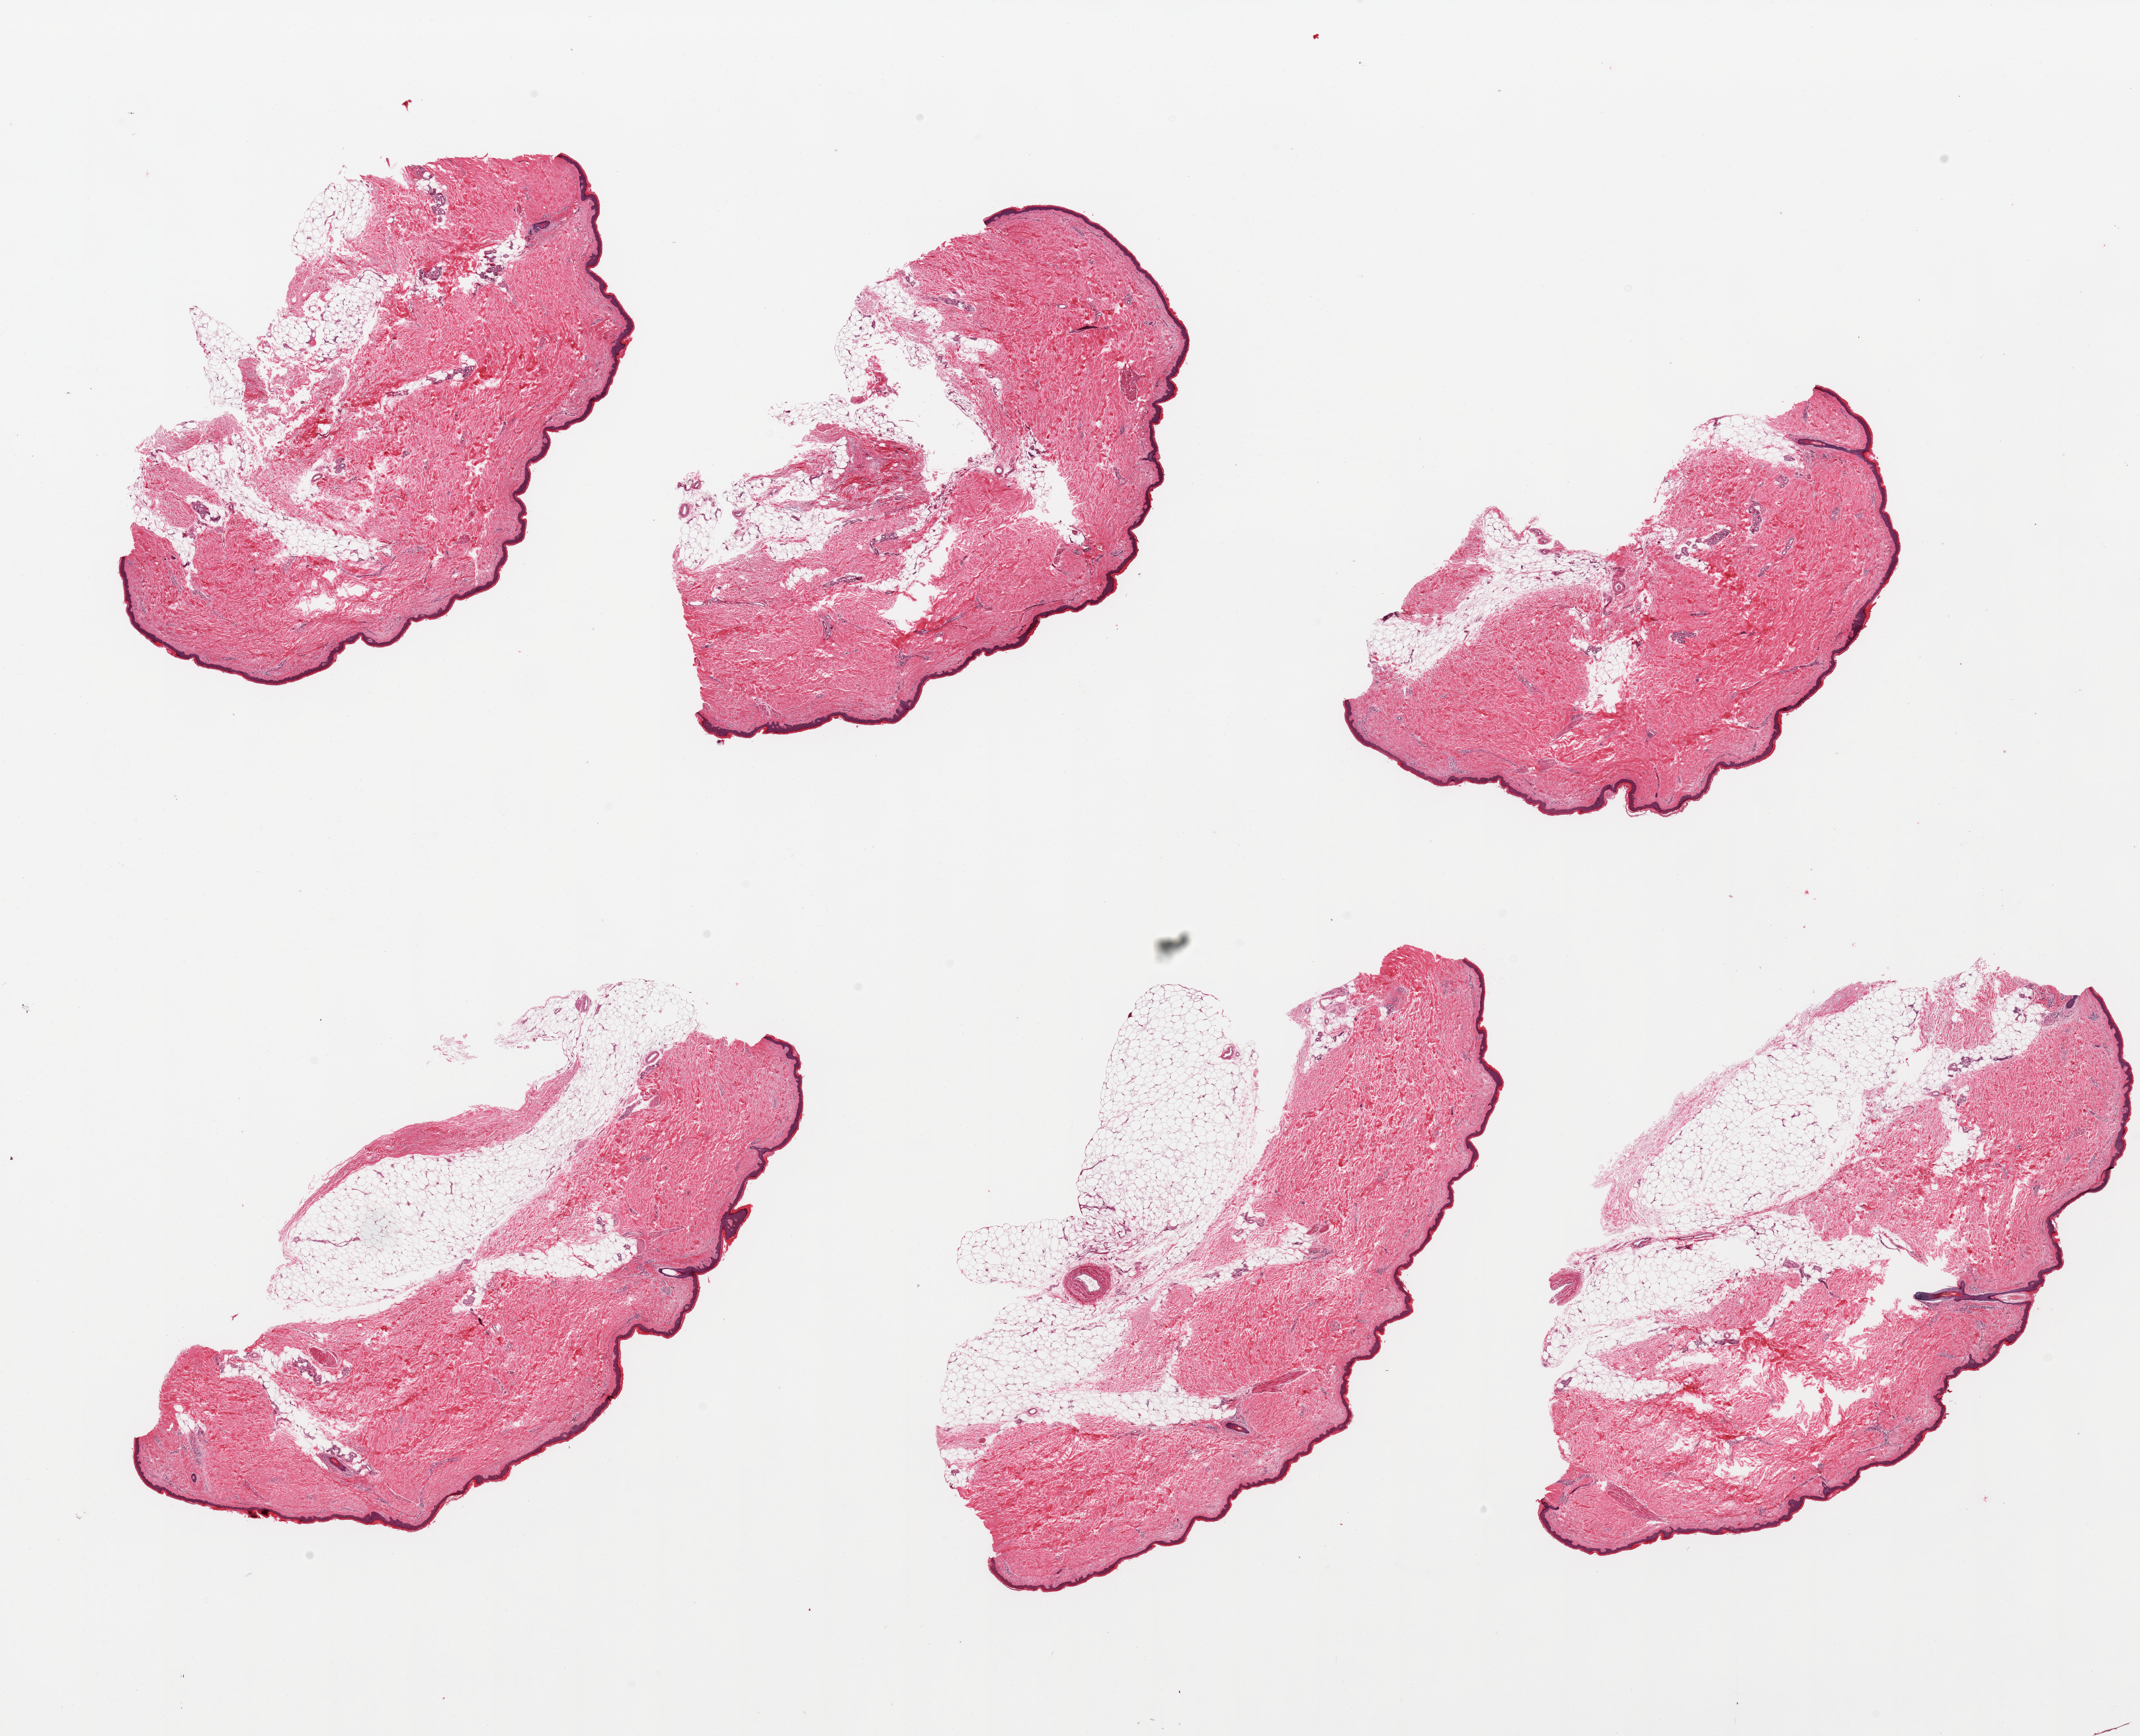
Digitized haematoxylin and eosin-stained section — low-resolution overview of the scanned area, about 25.6 x 20.8 mm; PAXgene-fixed paraffin-embedded (PFPE) section; section of skin of lower leg (target tissue); tissue donor sample.
• reviewer comment on this tissue sample: 6 pieces, adherent dermal fat up to ~1.5mm; squamous epithelium is ~50 microns